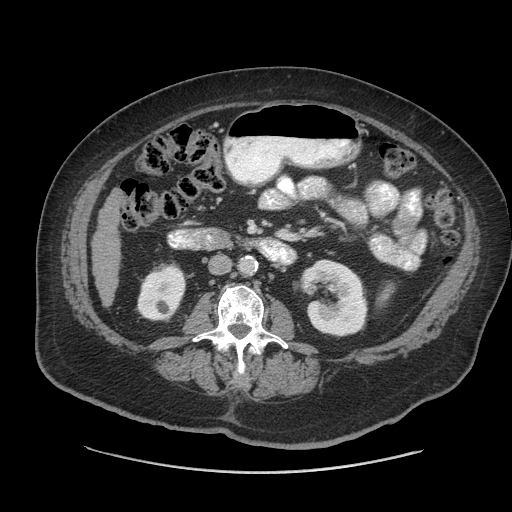
Contrast-enhanced abdominal CT (liver protocol), one axial slice. Slice 14 of 91 in the series (ordered by position). 140 kVp. Soft-tissue window (W 400 / L 40 HU). 2.5 mm slice thickness. 512 × 512 image matrix, field of view 420 × 420 mm. Case-level facts recorded for this patient, not image findings: diagnosis: hepatocellular carcinoma (patient treated with transarterial chemoembolisation; whether this scan precedes or follows treatment is not stated here); TNM stage (as recorded): Stage-I; Child-Pugh class: A; tumour differentiation: well differentiated; tumour nodularity: uninodular.
Annotated regions visible in this slice (semi-automatically segmented with operator editing):
- liver parenchyma outside the tumour (the mass and vessels are separate outlines, so this box may not span the whole liver): bounding box (x1, y1, x2, y2) in pixels: (92, 192, 120, 306)